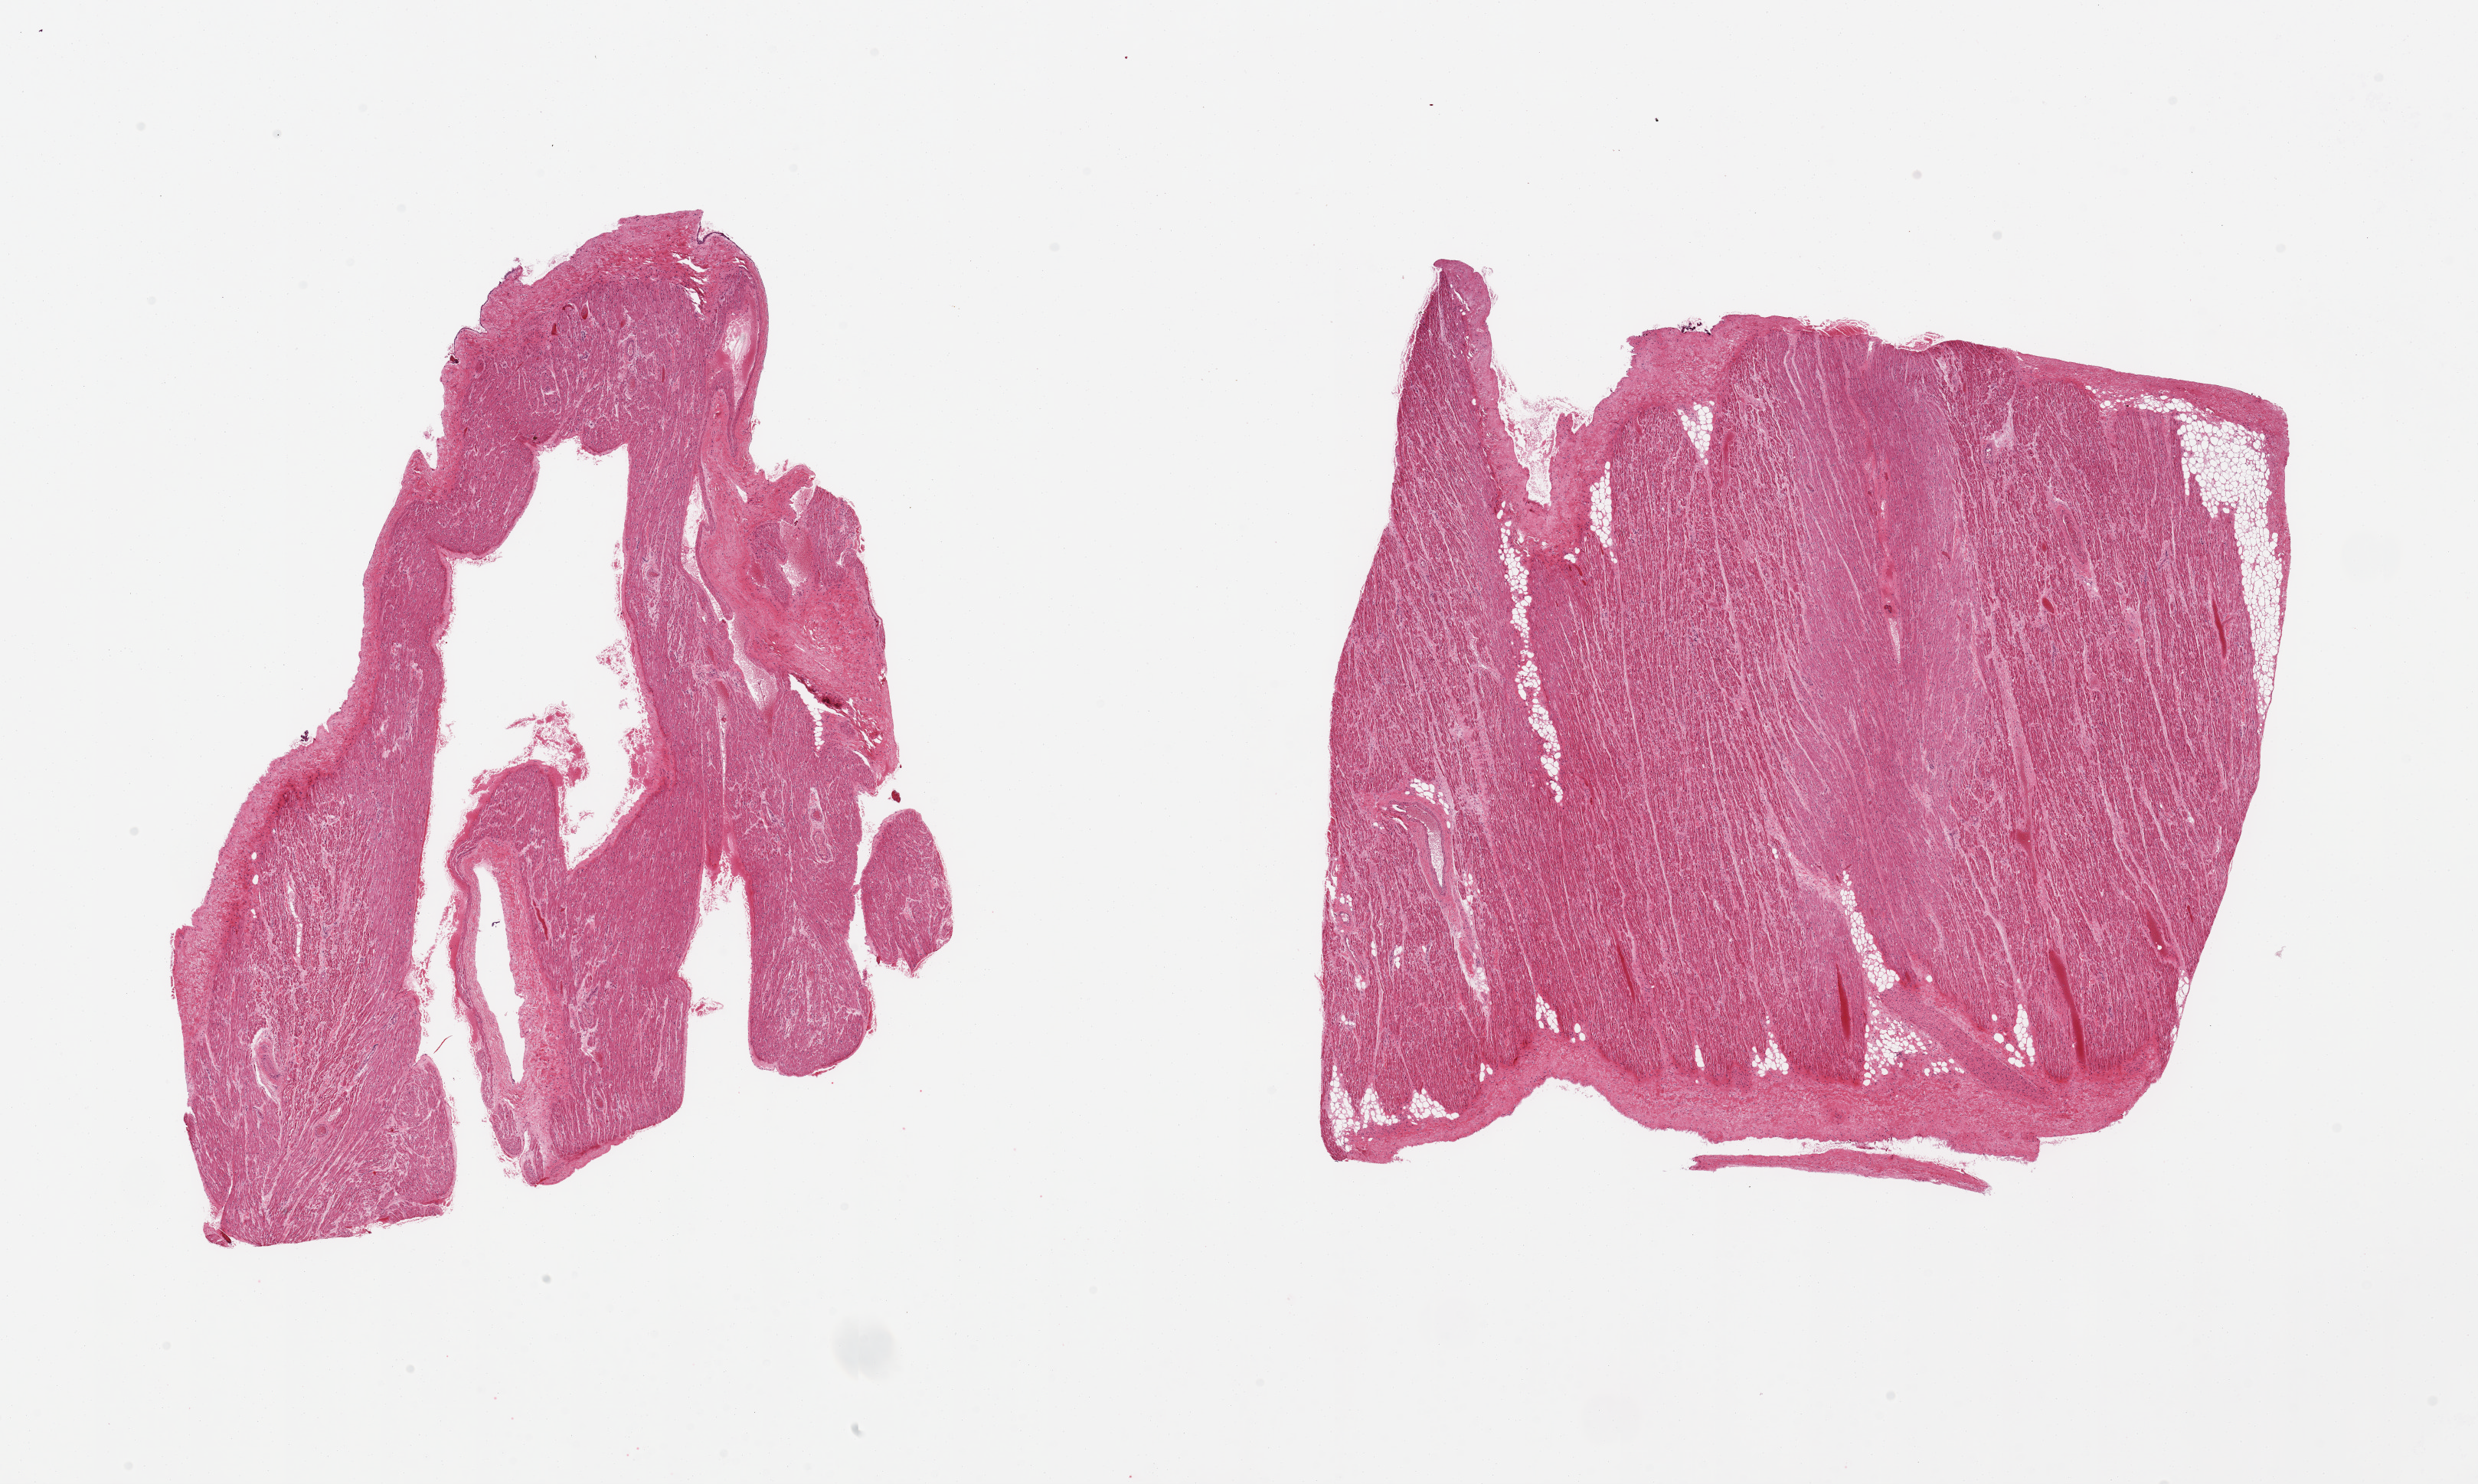
Haematoxylin and eosin whole-slide image, brightfield — whole scanned area (about 25.6 x 15.3 mm, slide scanned at 20x) shown as a low-resolution overview. PAXgene-fixed, paraffin-embedded tissue. Section of auricular appendage (target tissue). Tissue donor sample. Donor sex: male.
Reviewer comment on this tissue sample: 2 pieces, no abnormalities.